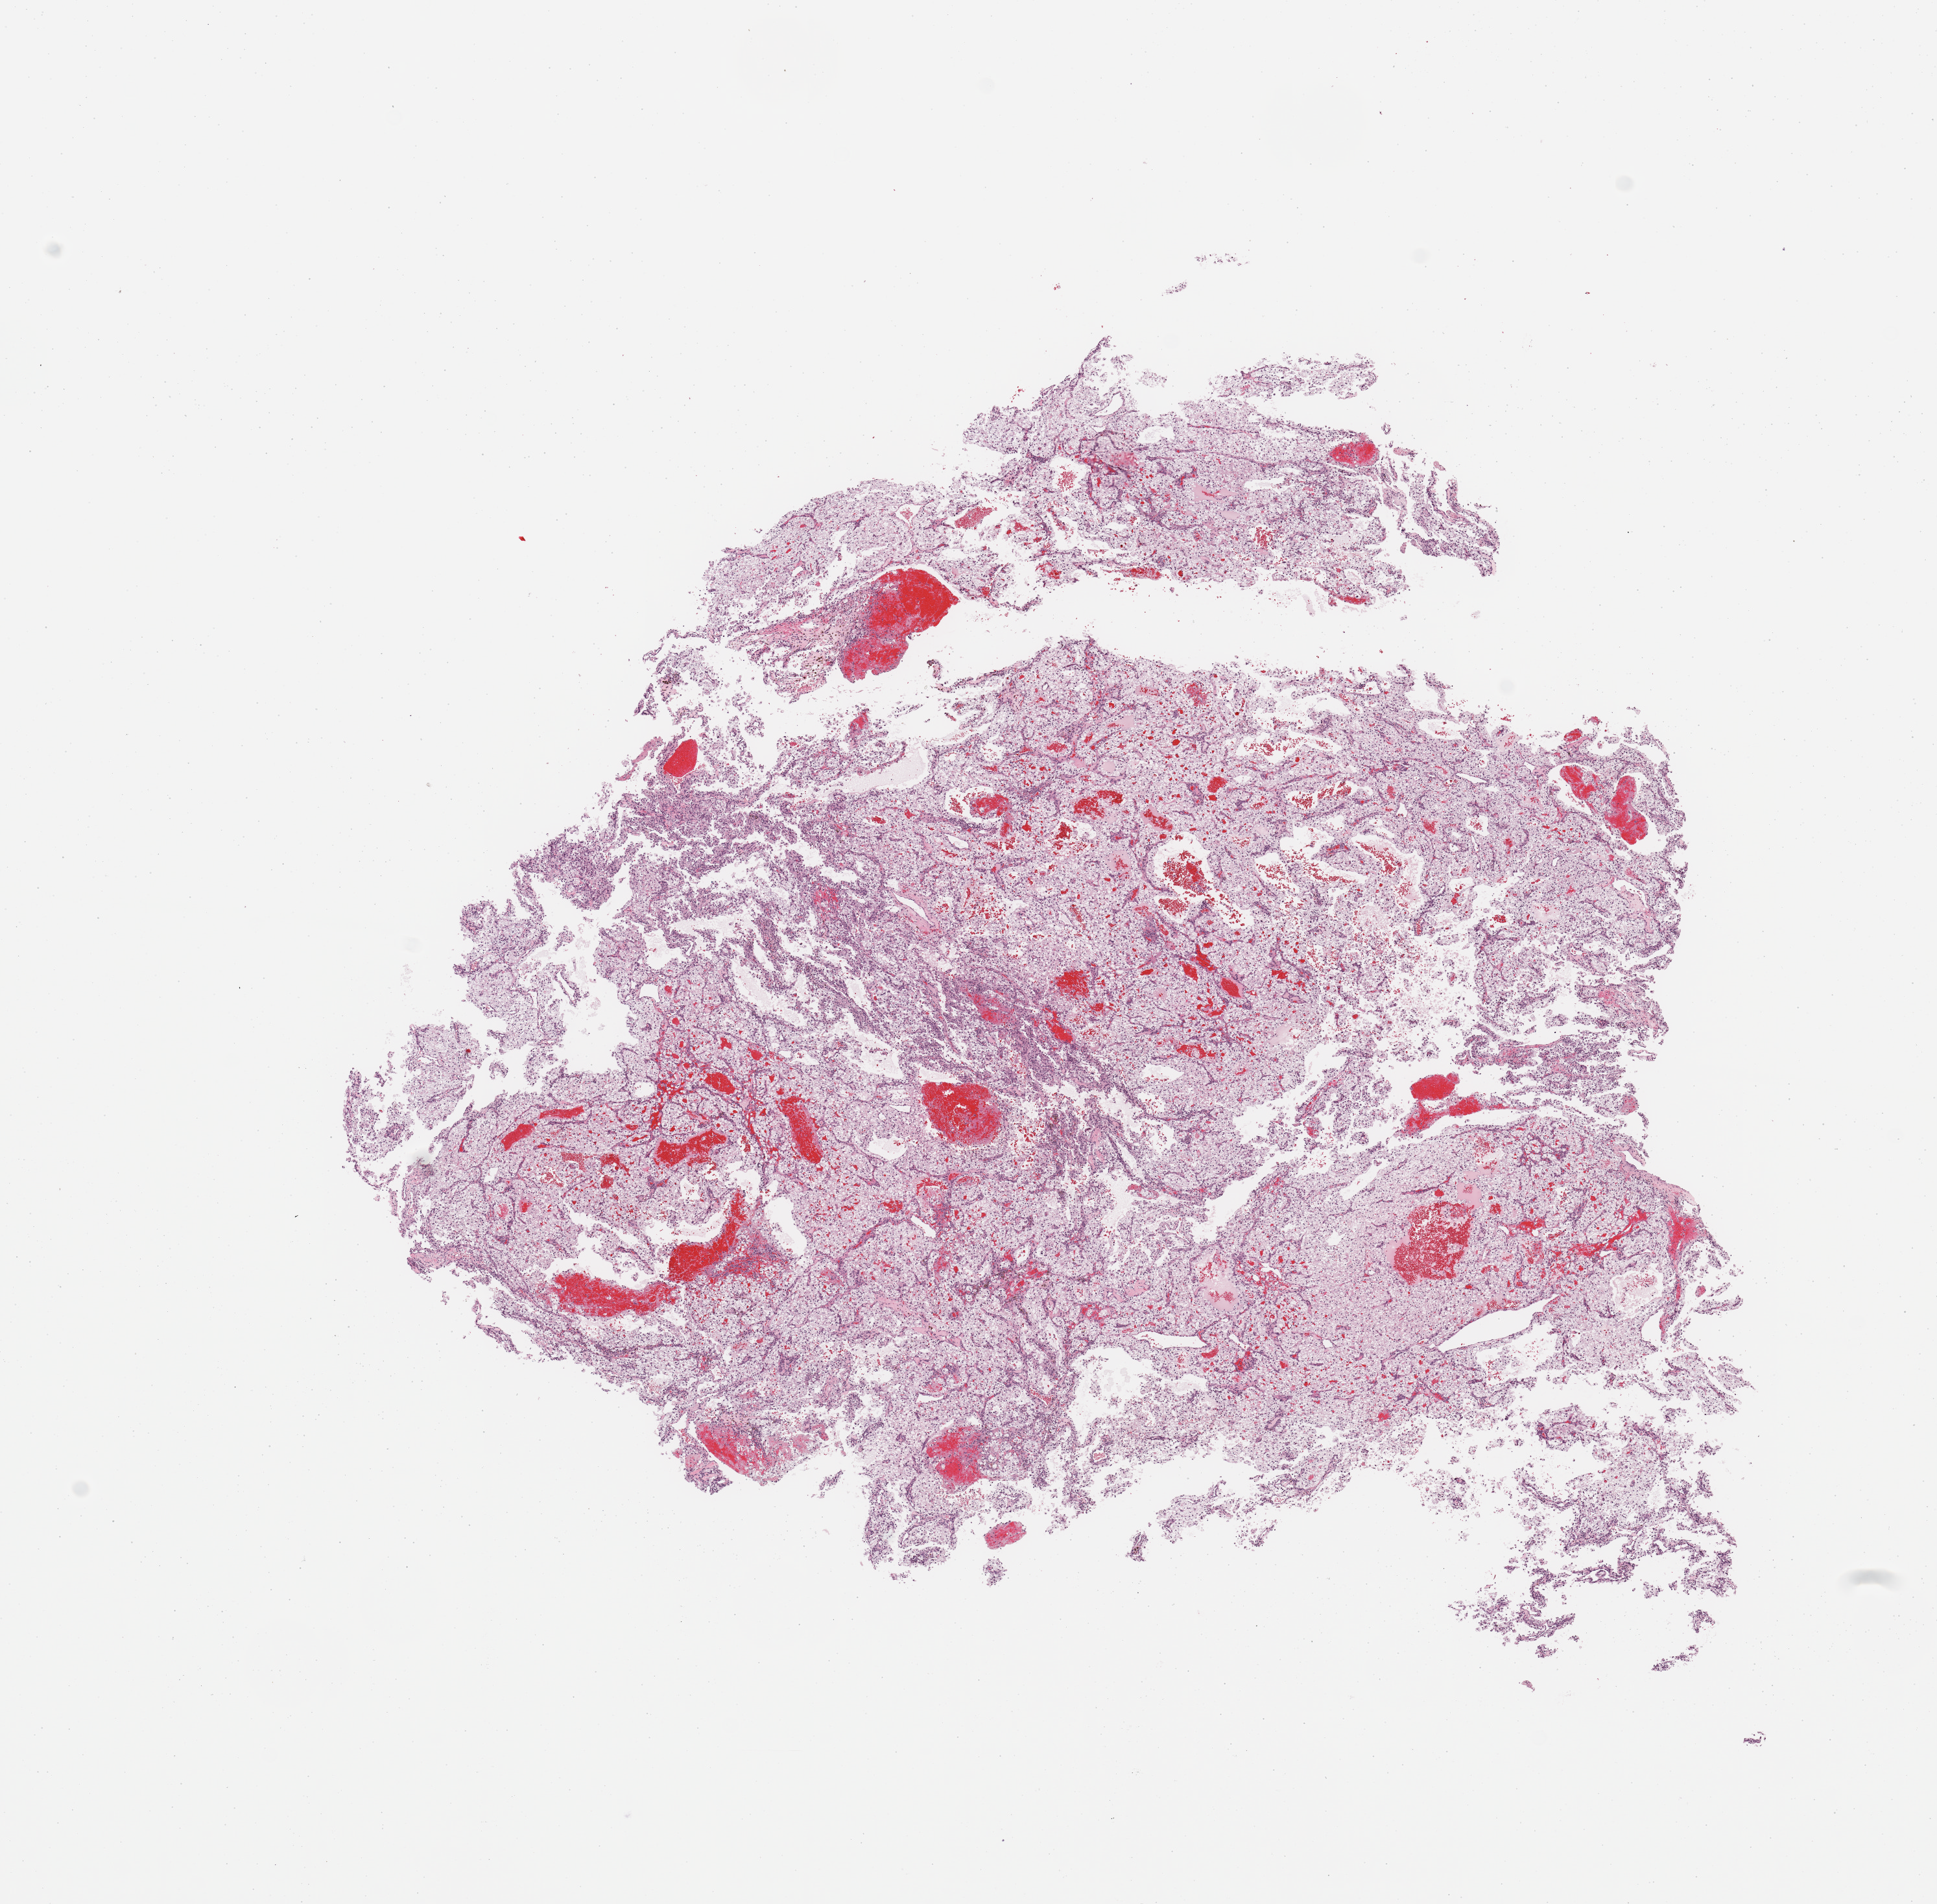
Whole-slide histology image, H&E — shown as a low-resolution overview of the whole scanned area (about 11.8 x 11.6 mm), tumour tissue sample, sampled site: kidney. 57-year-old female patient.
Diagnosis: Renal cell carcinoma, NOS.